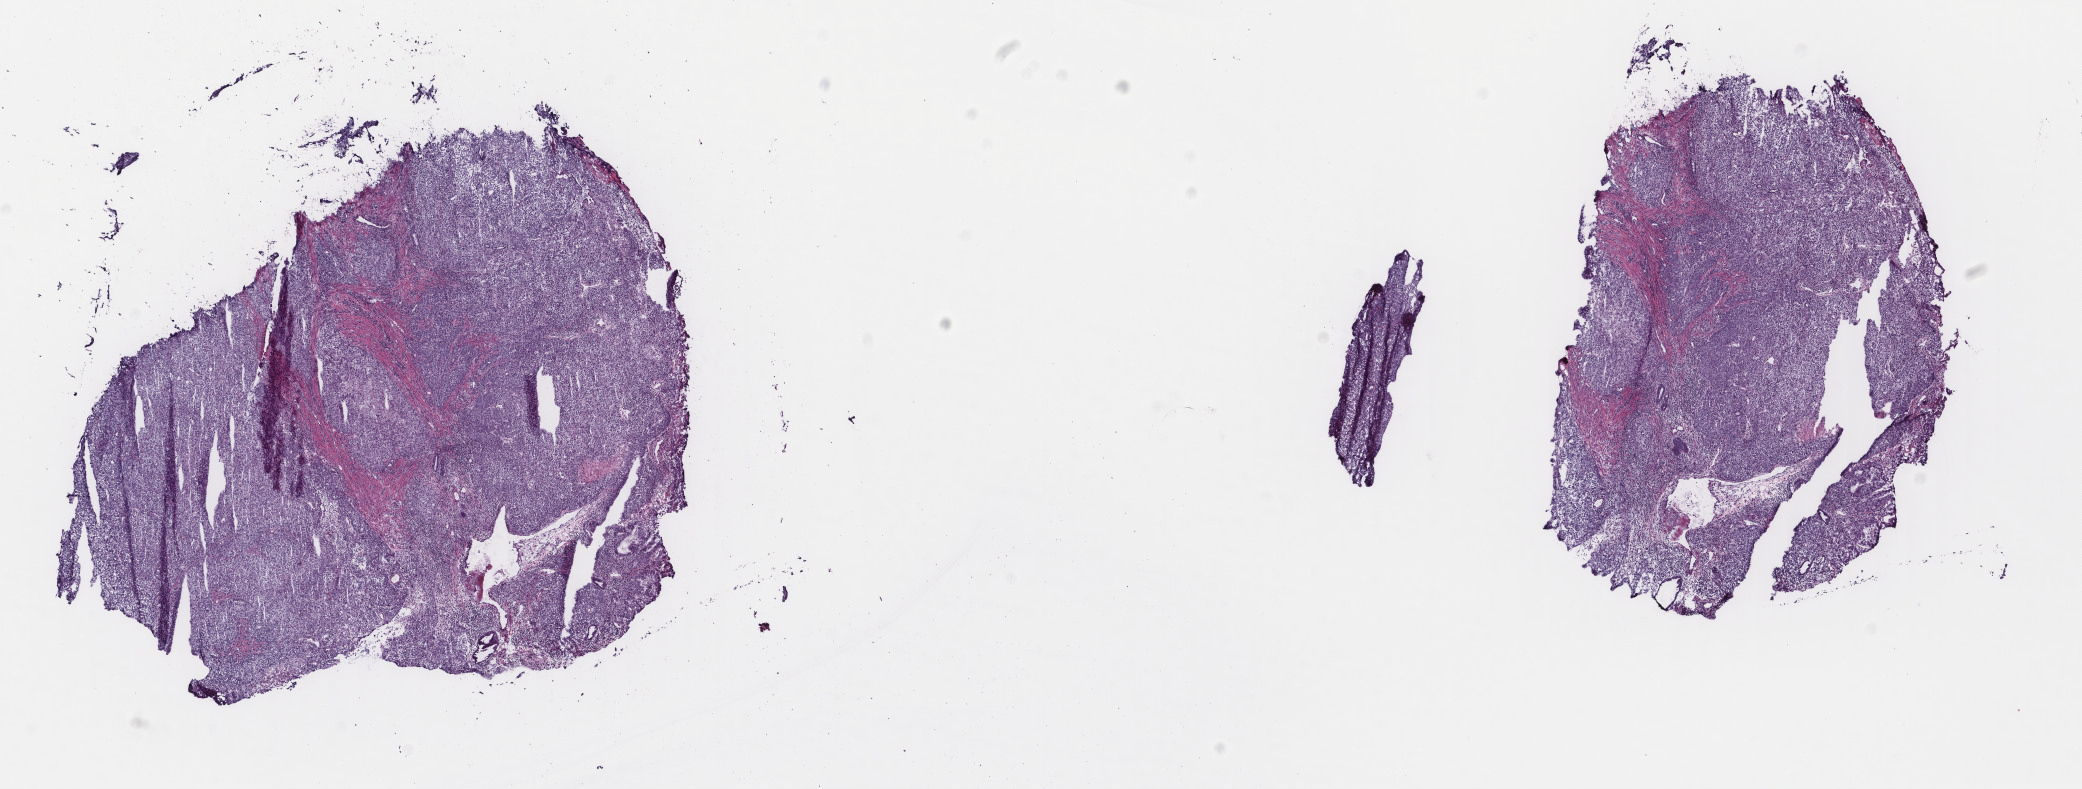
Digitized H&E tissue section (whole slide) — low-resolution overview of the scanned area, about 16.5 x 6.3 mm (acquisition: 40x scan), frozen section, sample: primary tumour, uterus. Female patient; age at initial diagnosis 78 years. Histologic grade: G3 (poorly differentiated). Slide review estimates, as recorded: tumour cells 82%, tumour nuclei 90%, normal cells 2%, stromal cells 10%, necrosis 6%. Inflammatory infiltration, as recorded: lymphocyte infiltration 15%, monocyte infiltration 2%, neutrophil infiltration 3%.
• FIGO stage: IIIC
• histologic diagnosis: Endometrioid adenocarcinoma, NOS (endometrium)
• lymph nodes positive (case pathology): 7 of 30 examined